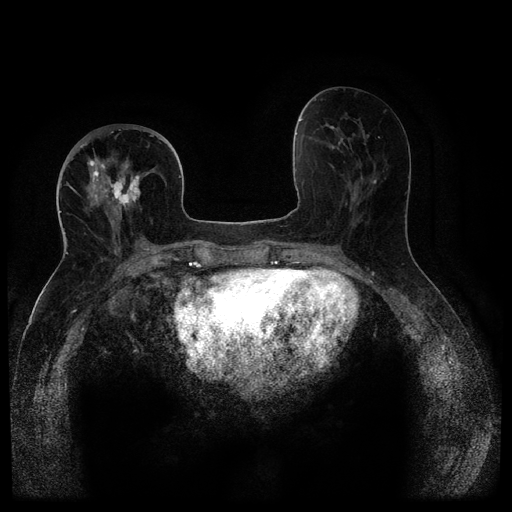
Breast MRI (dynamic contrast-enhanced, multi-phase), one axial slice; slice 47 of 116 in the series (ordered by position); dynamic contrast-enhanced series, time point 2 of 5 at this slice position (early post-contrast); 1.5 T; TE 2.6 ms, TR 5.4 ms; 2 mm slice thickness; 512 × 512 image matrix, field of view 340 × 340 mm. Patient: female, 68 years.
Annotated regions visible in this slice (semi-automatic segmentation, software-assisted and operator-edited):
- breast lesion (labelled 'tumour' in the annotation; benign lesions carry a separate 'benign' label): bounding box [x1, y1, x2, y2] px = [107, 169, 143, 213]
- breast lesion (labelled 'tumour' in the annotation; benign lesions carry a separate 'benign' label): [86, 154, 108, 208]